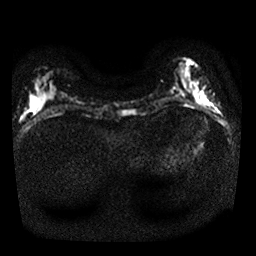
Breast MRI, one axial slice. Slice 6 of 25 in the series (ordered by position). Diffusion-weighted series; image 2 of 4 stored at this slice position (different b-values; order by instance number). 1.5 T. 4 mm slice thickness. 256 × 256 image matrix. Female patient.
Annotated regions visible in this slice (outlined manually by an expert reader):
- tumour on diffusion-weighted imaging: bounding box <203,96,206,103> (left, top, right, bottom; pixels)